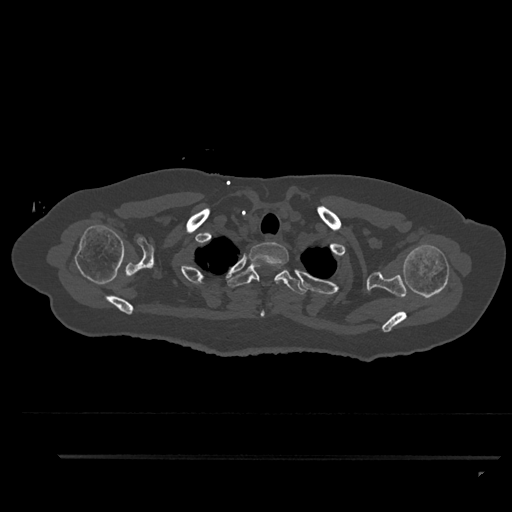
CT including the spine, one axial slice. Position 738 of 797 along the scan axis. Reconstruction kernel Br40s/3. Bone window (W 1800 / L 400 HU). 0.5 mm slice thickness. 512 × 512 image matrix, field of view 408 × 408 mm. Patient: female, 44 years. Case-level facts recorded for this patient, not image findings: primary cancer: renal; vertebrae with lytic lesions (as recorded): L1.
Structures marked on this image (semi-automatically segmented with operator editing):
- T1 vertebra: bounding box <249,242,289,317> (left, top, right, bottom; pixels)
- T2 vertebra: <227,263,307,295>